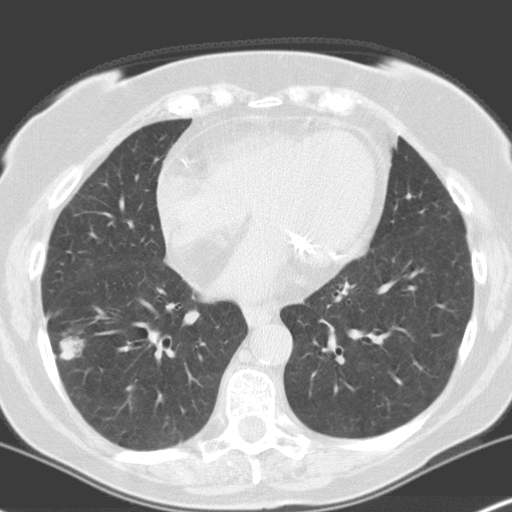
Low-dose screening chest CT, axial slice. Baseline annual screen. Lung window (W 1500 / L -600 HU). 3.2 mm slice thickness. 120 kVp. 512 × 512 image matrix, field of view 316 × 316 mm. Female participant, aged 70 years at enrolment. Current smoker at enrolment.
Expert reader's lesion annotation, box from (x=35, y=310) to (x=100, y=379) px. The screening reader recorded 4 non-calcified nodules or masses ≥4 mm on this exam (right lower lobe, right upper lobe, left upper lobe, left upper lobe); which of them this box marks is not recorded. Participant outcome: lung cancer diagnosed 28 days after this screen — adenocarcinoma, NOS, right lower lobe, moderately differentiated (G2), stage IV (AJCC 6th edition), 28 mm at pathology.